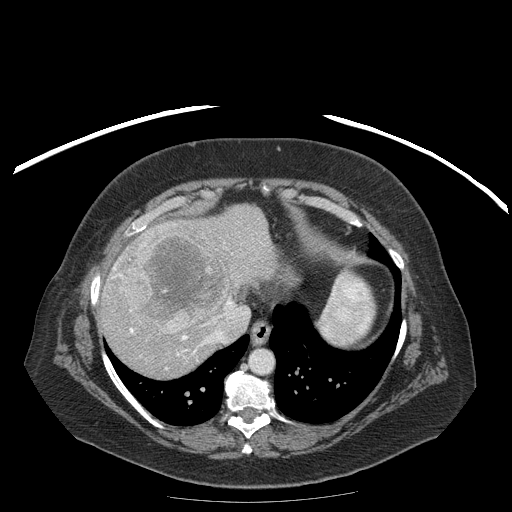
Contrast-enhanced abdominal CT (liver protocol), one axial slice; slice 153 of 204 in the series (ordered by position); reconstruction kernel STANDARD; soft-tissue window (W 400 / L 40 HU); 2.5 mm slice thickness; 512 × 512 image matrix, field of view 440 × 440 mm. Case-level facts recorded for this patient, not image findings: diagnosis: hepatocellular carcinoma (patient treated with transarterial chemoembolisation; whether this scan precedes or follows treatment is not stated here); TNM stage (as recorded): Stage-IIIB; Child-Pugh class: A; tumour differentiation: well differentiated; tumour nodularity: uninodular.
Annotated regions visible in this slice (semi-automatic segmentation, software-assisted and operator-edited):
- liver parenchyma outside the tumour (the mass and vessels are separate outlines, so this box may not span the whole liver): bounding box (x1, y1, x2, y2) in pixels: (98, 204, 278, 378)
- mass: (127, 233, 228, 334)
- liver vessels: (112, 236, 248, 355)